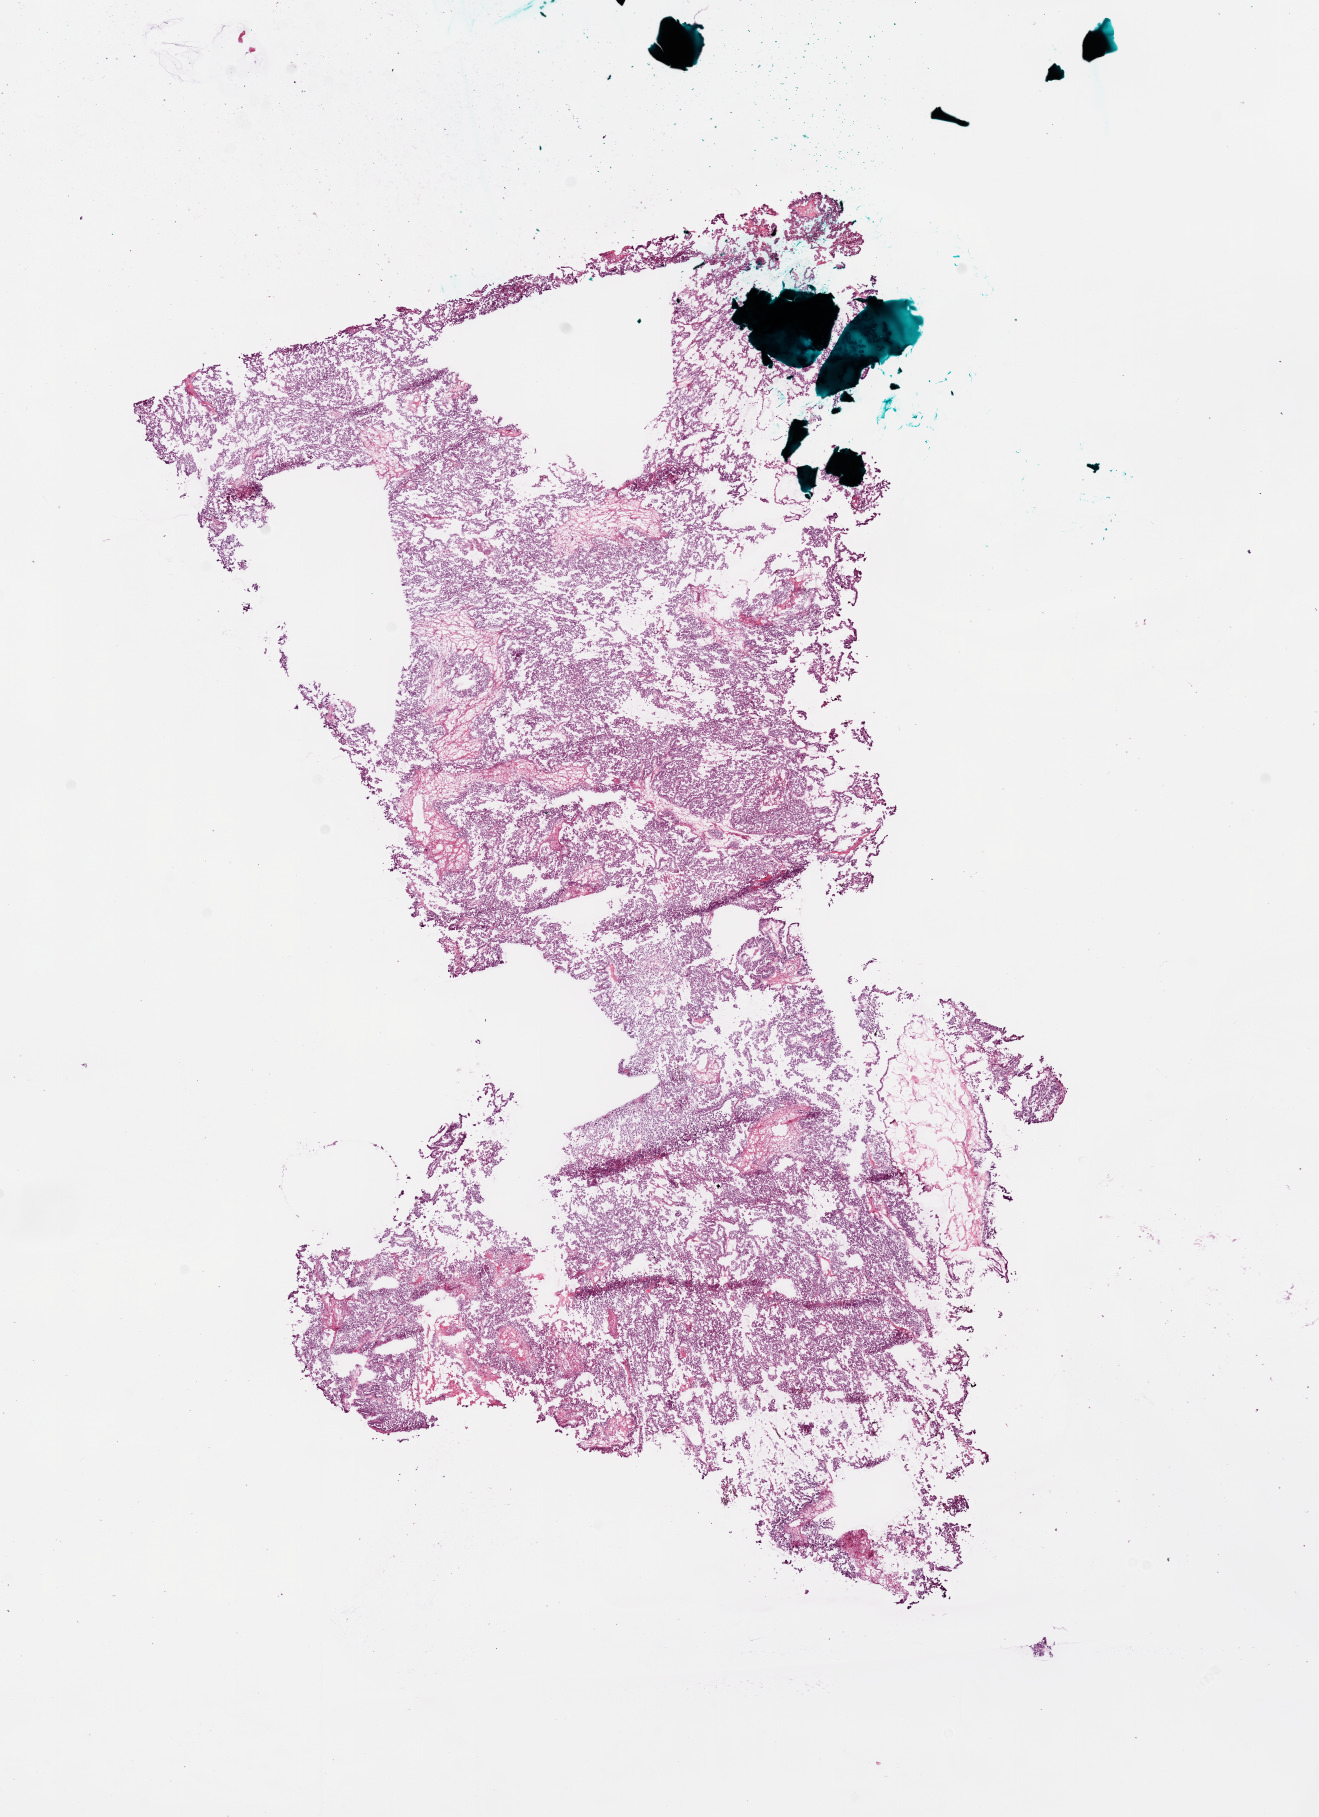
Digitized H&E tissue section (whole slide), low-resolution overview of the scanned area, about 10.6 x 14.7 mm. Frozen section from the bottom of the tissue portion. Sample: primary tumour, ovary. Female, age 58 years at initial diagnosis. Histologic grade: G3 (poorly differentiated). Slide review estimates, as recorded: tumour cells 89%, tumour nuclei 90%, normal cells 10%, stromal cells 0%, necrosis 1%.
FIGO stage: IIIC. Pathologic diagnosis: Serous cystadenocarcinoma, NOS.